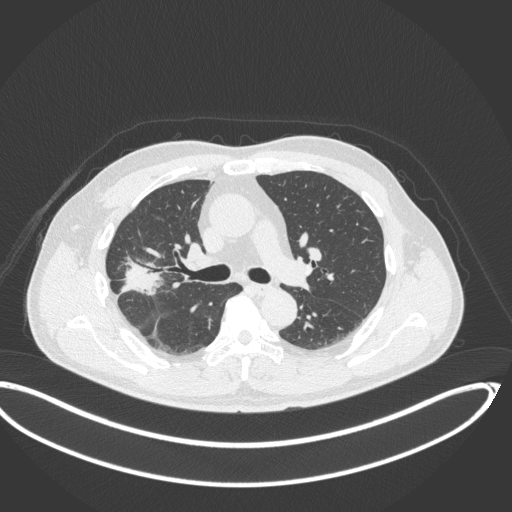
Chest CT, one axial slice. Position 212 of 341 along the scan axis. Reconstruction kernel B31f. Lung window (W 1500 / L -600 HU). 512 × 512 image matrix, field of view 439 × 439 mm. Male patient, age 63 years. From the clinical record (not read from this slice): clinical TNM (as recorded): T1c N0 M0.
Outlined on this slice (rectangle marked by the reading radiologist):
- lung tumour (recorded histology: adenocarcinoma): bounding box <119,253,167,299> (left, top, right, bottom; pixels)